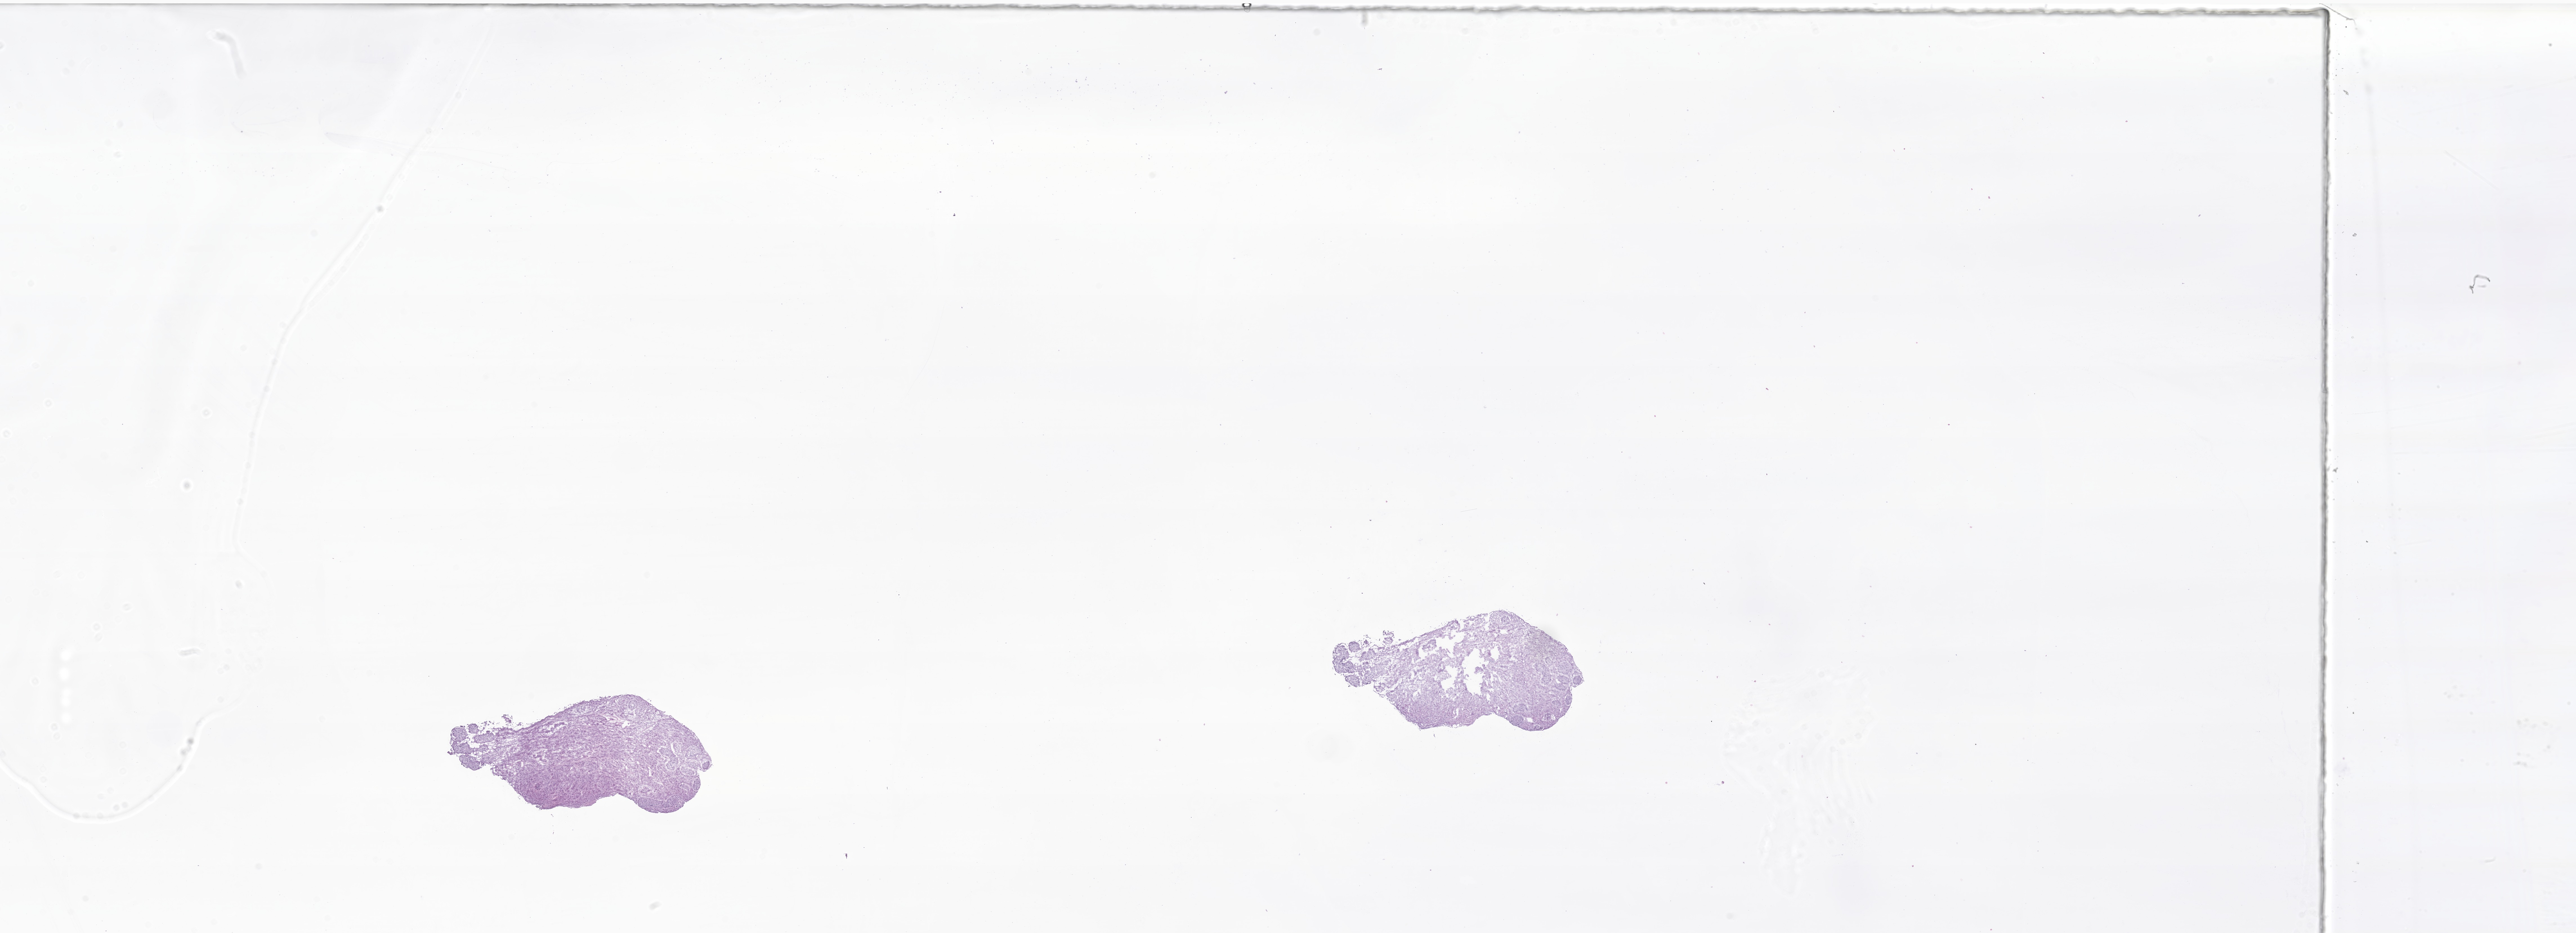
Whole-slide image, haematoxylin and eosin stain of tumor tissue from the testis, shown as a low-resolution overview of the whole scanned area (about 38.6 x 14.0 mm); frozen section. Patient: male, age 62 months (5 years 2 months).
Diagnosis: Leydig cell tumor of testis, NOS.